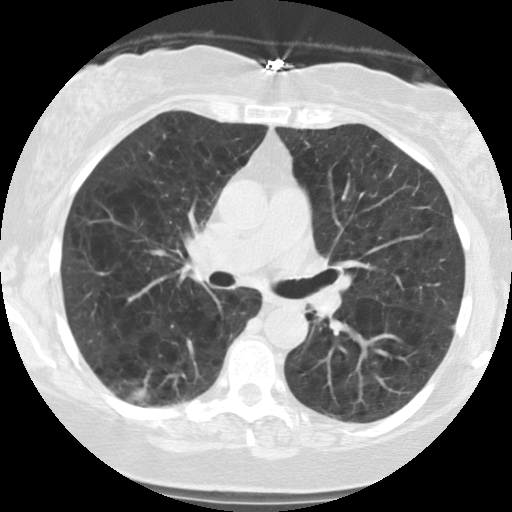
Low-dose screening chest CT, one axial slice; position 68 of 122 along the scan axis; reconstruction kernel STANDARD; lung window (W 1500 / L -600 HU); 2.5 mm slice thickness; 512 × 512 image matrix.
Structures marked on this image (outlined manually by an expert reader):
- lesion 1 (tumor, lower lobe of right lung): bounding box (x1, y1, x2, y2) in pixels: (129, 385, 147, 404)